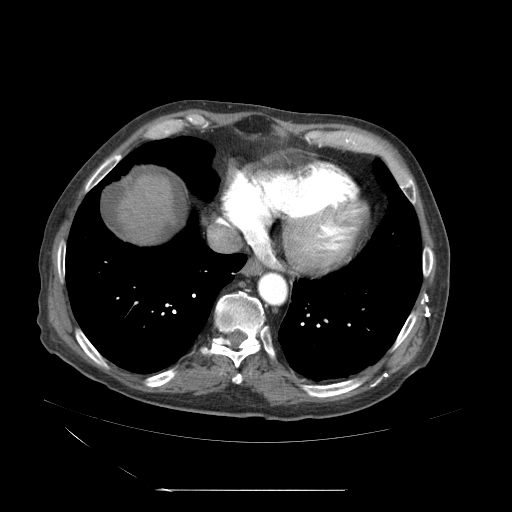
Contrast-enhanced abdominal CT (liver protocol), one axial slice; position 58 of 71 along the scan axis; 120 kVp; soft-tissue window (W 400 / L 40 HU); 2.5 mm slice thickness; 512 × 512 image matrix. From the clinical record (not read from this slice): diagnosis: hepatocellular carcinoma (patient treated with transarterial chemoembolisation; whether this scan precedes or follows treatment is not stated here); TNM stage (as recorded): Stage-II; Child-Pugh class: A.
Outlined on this slice (semi-automatically segmented with operator editing):
- abdominal aorta: box from (x=259, y=271) to (x=288, y=306) px
- liver parenchyma outside the tumour (the mass and vessels are separate outlines, so this box may not span the whole liver): (x=131, y=166)–(x=193, y=248)